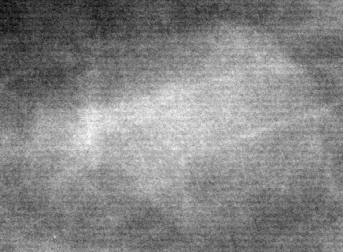
Crop from a digitized film mammogram around one marked abnormality; right breast; CC view; BI-RADS breast density category 1 (scale 1–4).
Marked abnormality: mass, shape round, margins circumscribed; BI-RADS assessment category 2; subtlety rating 5 on a 1 (subtle) to 5 (obvious) scale; pathology result (as recorded, not read from the image): benign.